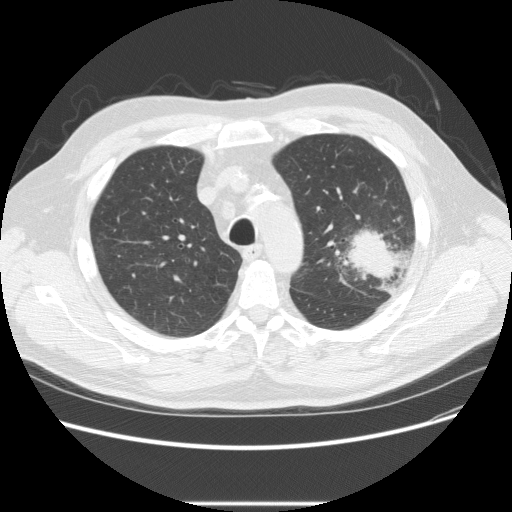
Chest CT (low-dose screening protocol), one axial image. First (baseline) screen. Lung window (W 1500 / L -600 HU). 2.5 mm slice thickness. Standard (soft-tissue) reconstruction kernel (STANDARD). 512 × 512 image matrix, field of view 380 × 380 mm. Male, age 73 years at enrolment. Former smoker at enrolment.
Lesion marked by an expert reader, bounding box [x1, y1, x2, y2] px = [332, 215, 416, 286]. The screening reader recorded 2 non-calcified nodules or masses ≥4 mm on this exam; which of them this box marks is not recorded. Official screen result: positive, change unspecified: nodule(s) >= 4 mm or enlarging nodule(s), mass(es), or other non-specific abnormalities suspicious for lung cancer. Lung cancer was diagnosed 11 days after this screen: bronchiolo-alveolar adenocarcinoma, NOS, other location, well differentiated (G1), stage IV (AJCC 6th edition).